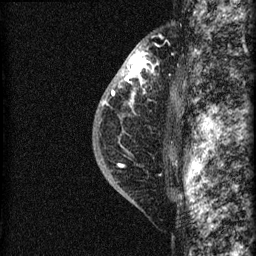
Breast MRI (dynamic contrast-enhanced), one sagittal slice; dynamic contrast-enhanced series, image 2 of 3 at this slice position (ordered by acquisition); 1.5 T; TE 4.2 ms, TR 22.7 ms; 1.5 mm slice thickness; 256 × 256 image matrix. Female patient, age 48 years. From the clinical record (not read from this slice): setting: breast cancer imaged before/during neoadjuvant chemotherapy; receptor status: triple-negative.
Structures marked on this image (semi-automatic segmentation, software-assisted and operator-edited):
- analysis volume of interest (the breast-tissue region the enhancement analysis was run in; not a lesion): bounding box <115,34,169,162> (left, top, right, bottom; pixels)
- tumour enhancement mask (voxels above the 90 % enhancement threshold inside the analysis volume of interest): <119,50,151,104>